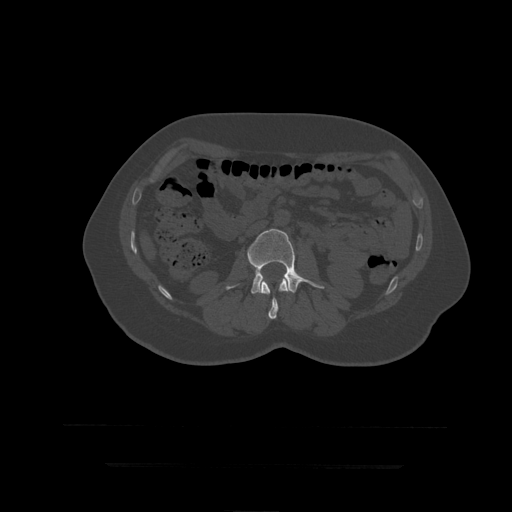
CT including the spine, one axial slice; position 133 of 399 along the scan axis; reconstruction kernel STANDARD; 120 kVp; bone window (W 1800 / L 400 HU); 1.25 mm slice thickness; 512 × 512 image matrix, field of view 450 × 450 mm. Patient age 41 years. Case-level facts recorded for this patient, not image findings: primary cancer: breast.
Annotated regions visible in this slice (semi-automatic segmentation, software-assisted and operator-edited):
- L2 vertebra: bounding box [x1, y1, x2, y2] px = [261, 277, 289, 319]
- L3 vertebra: [226, 229, 325, 294]